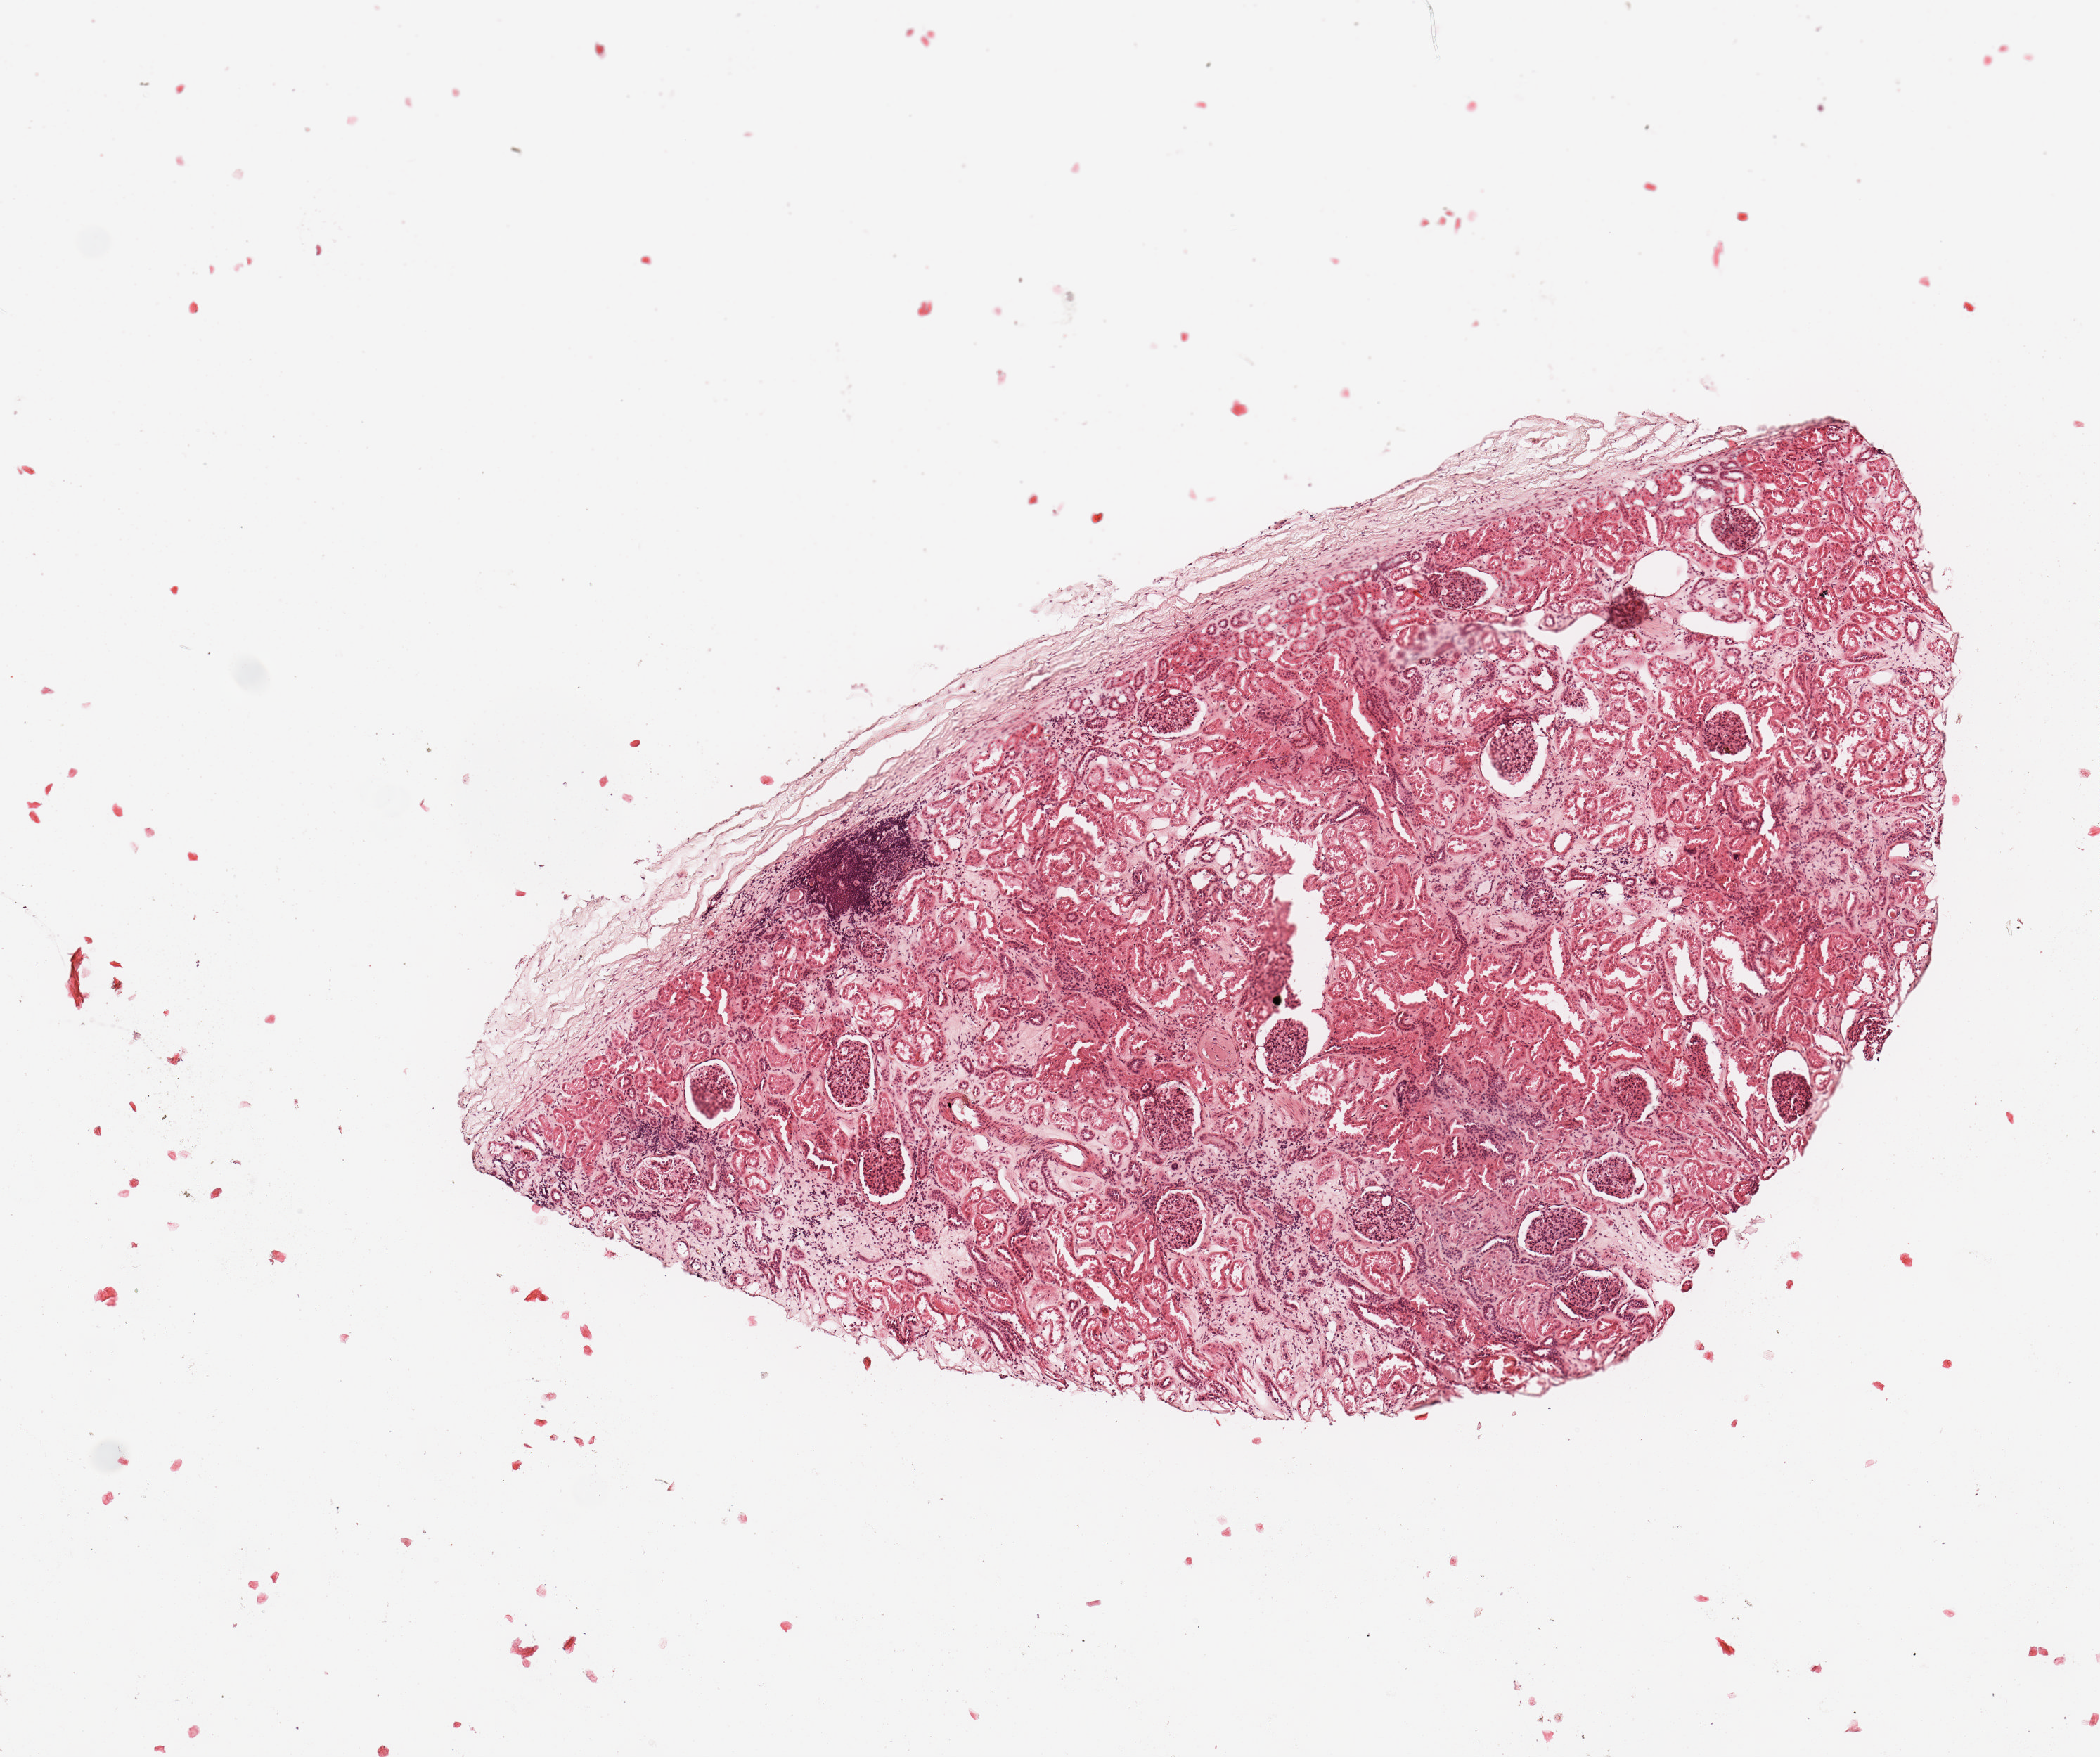
H&E whole-slide image, whole scanned area (about 5.9 x 4.9 mm) shown as a low-resolution overview. Normal (non-tumour) tissue sample, sampled site: kidney. Patient: male, age 68 years.
This section: normal (non-tumour) tissue from the same patient. Patient diagnosis: Renal cell carcinoma, NOS.